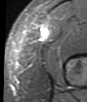
MRI of an extremity soft-tissue mass, one axial slice. Slice 10 of 48 in the series (ordered by position). STIR. MR volume resampled by the dataset authors to the PET/CT grid (not the native acquisition matrix). 87 × 102 image matrix, field of view 85 × 100 mm. Female patient. Case-level facts recorded for this patient, not image findings: histological type: synovial sarcoma; grade: intermediate; site of the primary tumour: right thigh.
Structures marked on this image (expert contour drawn on MRI and transferred to this co-registered scan by the dataset authors):
- gross tumour volume including surrounding oedema: bounding box (x1, y1, x2, y2) in pixels: (42, 29, 48, 39)
- gross tumour volume (mass): (40, 29, 48, 39)